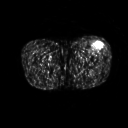
FDG PET of an extremity soft-tissue mass (from a PET/CT study), one axial slice; slice 221 of 267 in the series (ordered by position); 3.27 mm slice thickness; 128 × 128 image matrix, field of view 500 × 500 mm. Male patient, age 64 years. From the clinical record (not read from this slice): histological type: extraskeletal osteosarcoma; grade: high; site of the primary tumour: thigh.
Annotated regions visible in this slice (expert contour drawn on MRI and transferred to this co-registered scan by the dataset authors):
- gross tumour volume (mass): box from (x=94, y=43) to (x=101, y=51) px